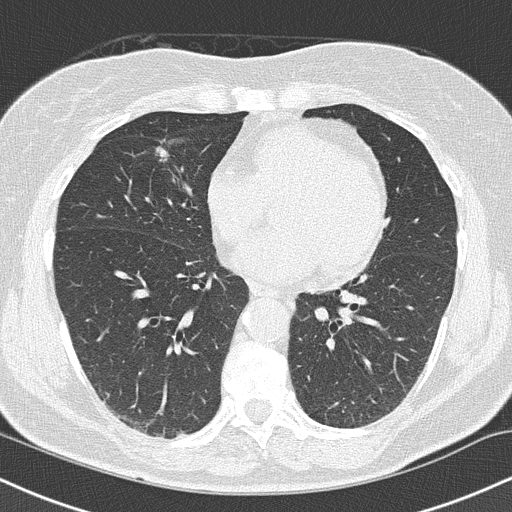
Chest CT (low-dose screening protocol), one axial image, baseline annual screen, lung window (W 1500 / L -600 HU), 2 mm slice thickness, 120 kVp, slice 84 of 145 in the series, 512 × 512 image matrix, field of view 320 × 320 mm. Female participant, aged 66 years at enrolment. Current smoker at enrolment.
Expert reader's lesion annotation, bounding box [x1, y1, x2, y2] px = [144, 134, 176, 167]. Reader record for this screening exam (exam-level; its link to the box is not recorded): non-calcified nodule or mass ≥4 mm, right lower lobe, 10 × 8 mm, smooth margins, soft tissue attenuation. Official screen result: positive, change unspecified: nodule(s) >= 4 mm or enlarging nodule(s), mass(es), or other non-specific abnormalities suspicious for lung cancer. Later outcome: lung cancer diagnosed 96 days after this screen — squamous cell carcinoma, keratinizing, NOS, right upper lobe, right middle lobe, poorly differentiated (G3), stage IA (AJCC 6th edition), 14 mm at pathology.